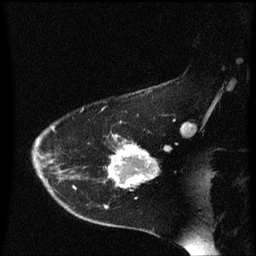
Breast MRI (dynamic contrast-enhanced), one sagittal slice. Slice 44 of 60 in the series (ordered by position). Dynamic contrast-enhanced series, image 2 of 3 at this slice position (ordered by acquisition). 1.5 T. TE 4.2 ms, TR 8.4 ms. 2 mm slice thickness. 256 × 256 image matrix, field of view 200 × 200 mm. Patient: female, 54 years. Case-level facts recorded for this patient, not image findings: setting: breast cancer imaged before/during neoadjuvant chemotherapy; receptor status: HR-positive, HER2-negative.
Annotated regions visible in this slice (semi-automatic segmentation, software-assisted and operator-edited):
- analysis volume of interest (the breast-tissue region the enhancement analysis was run in; not a lesion): box from (x=106, y=132) to (x=159, y=189) px
- tumour enhancement mask (voxels above the 70 % enhancement threshold inside the analysis volume of interest): (x=111, y=144)–(x=158, y=189)